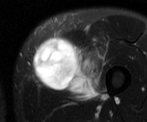
MRI of an extremity soft-tissue mass, one axial slice. Slice 17 of 52 in the series (ordered by position). T2-weighted fat-saturated. MR volume resampled by the dataset authors to the PET/CT grid (not the native acquisition matrix). 147 × 122 image matrix, field of view 144 × 119 mm. Male patient. From the clinical record (not read from this slice): histological type: pleiomorphic liposarcoma; grade: high; site of the primary tumour: left thigh.
Annotated regions visible in this slice (expert contour drawn on MRI and transferred to this co-registered scan by the dataset authors):
- gross tumour volume including surrounding oedema: bounding box [x1, y1, x2, y2] px = [32, 32, 102, 100]
- gross tumour volume (mass): [32, 34, 95, 93]